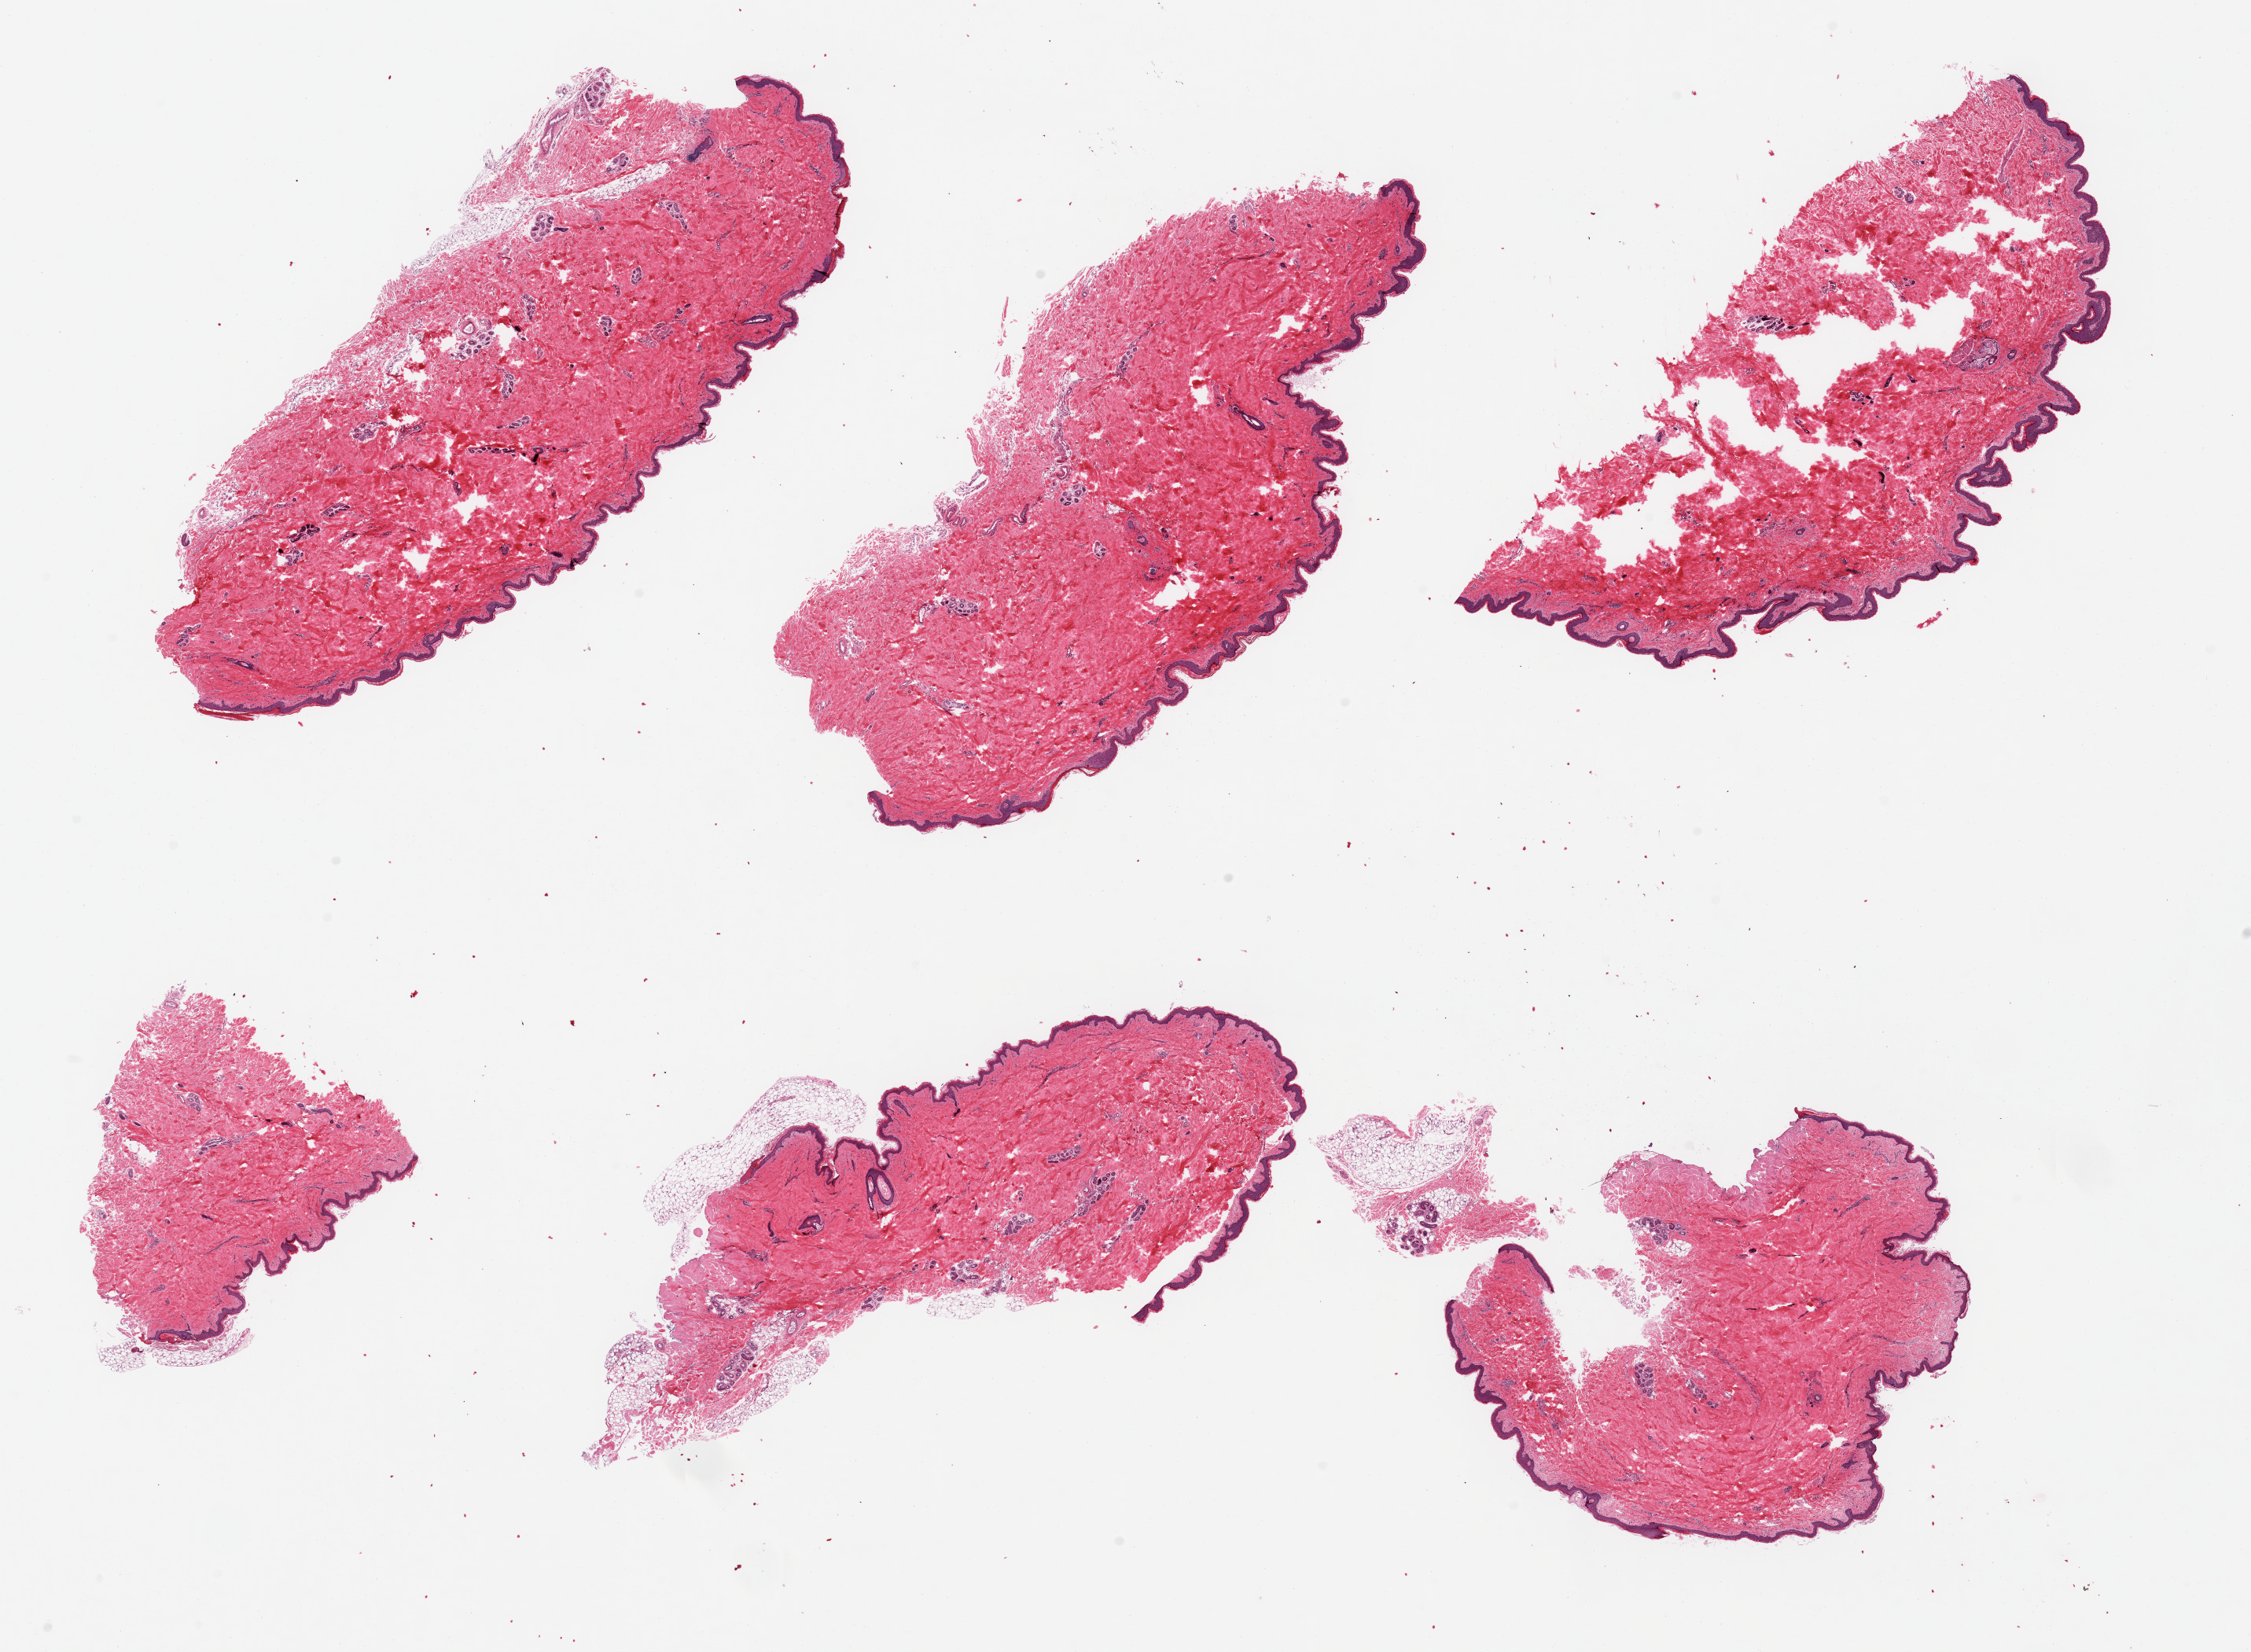
Whole-slide image, haematoxylin and eosin stain, brightfield, shown as a low-resolution overview of the whole scanned area (about 22.6 x 16.6 mm, from a 20x scan); PAXgene-fixed paraffin-embedded (PFPE) section; section of skin of suprapubic region (target tissue); donor tissue sample. Female donor.
- reviewer comment on this tissue sample: 6 pieces, trace adherent dermal fat, squamous epithelium is ~50-60 microns